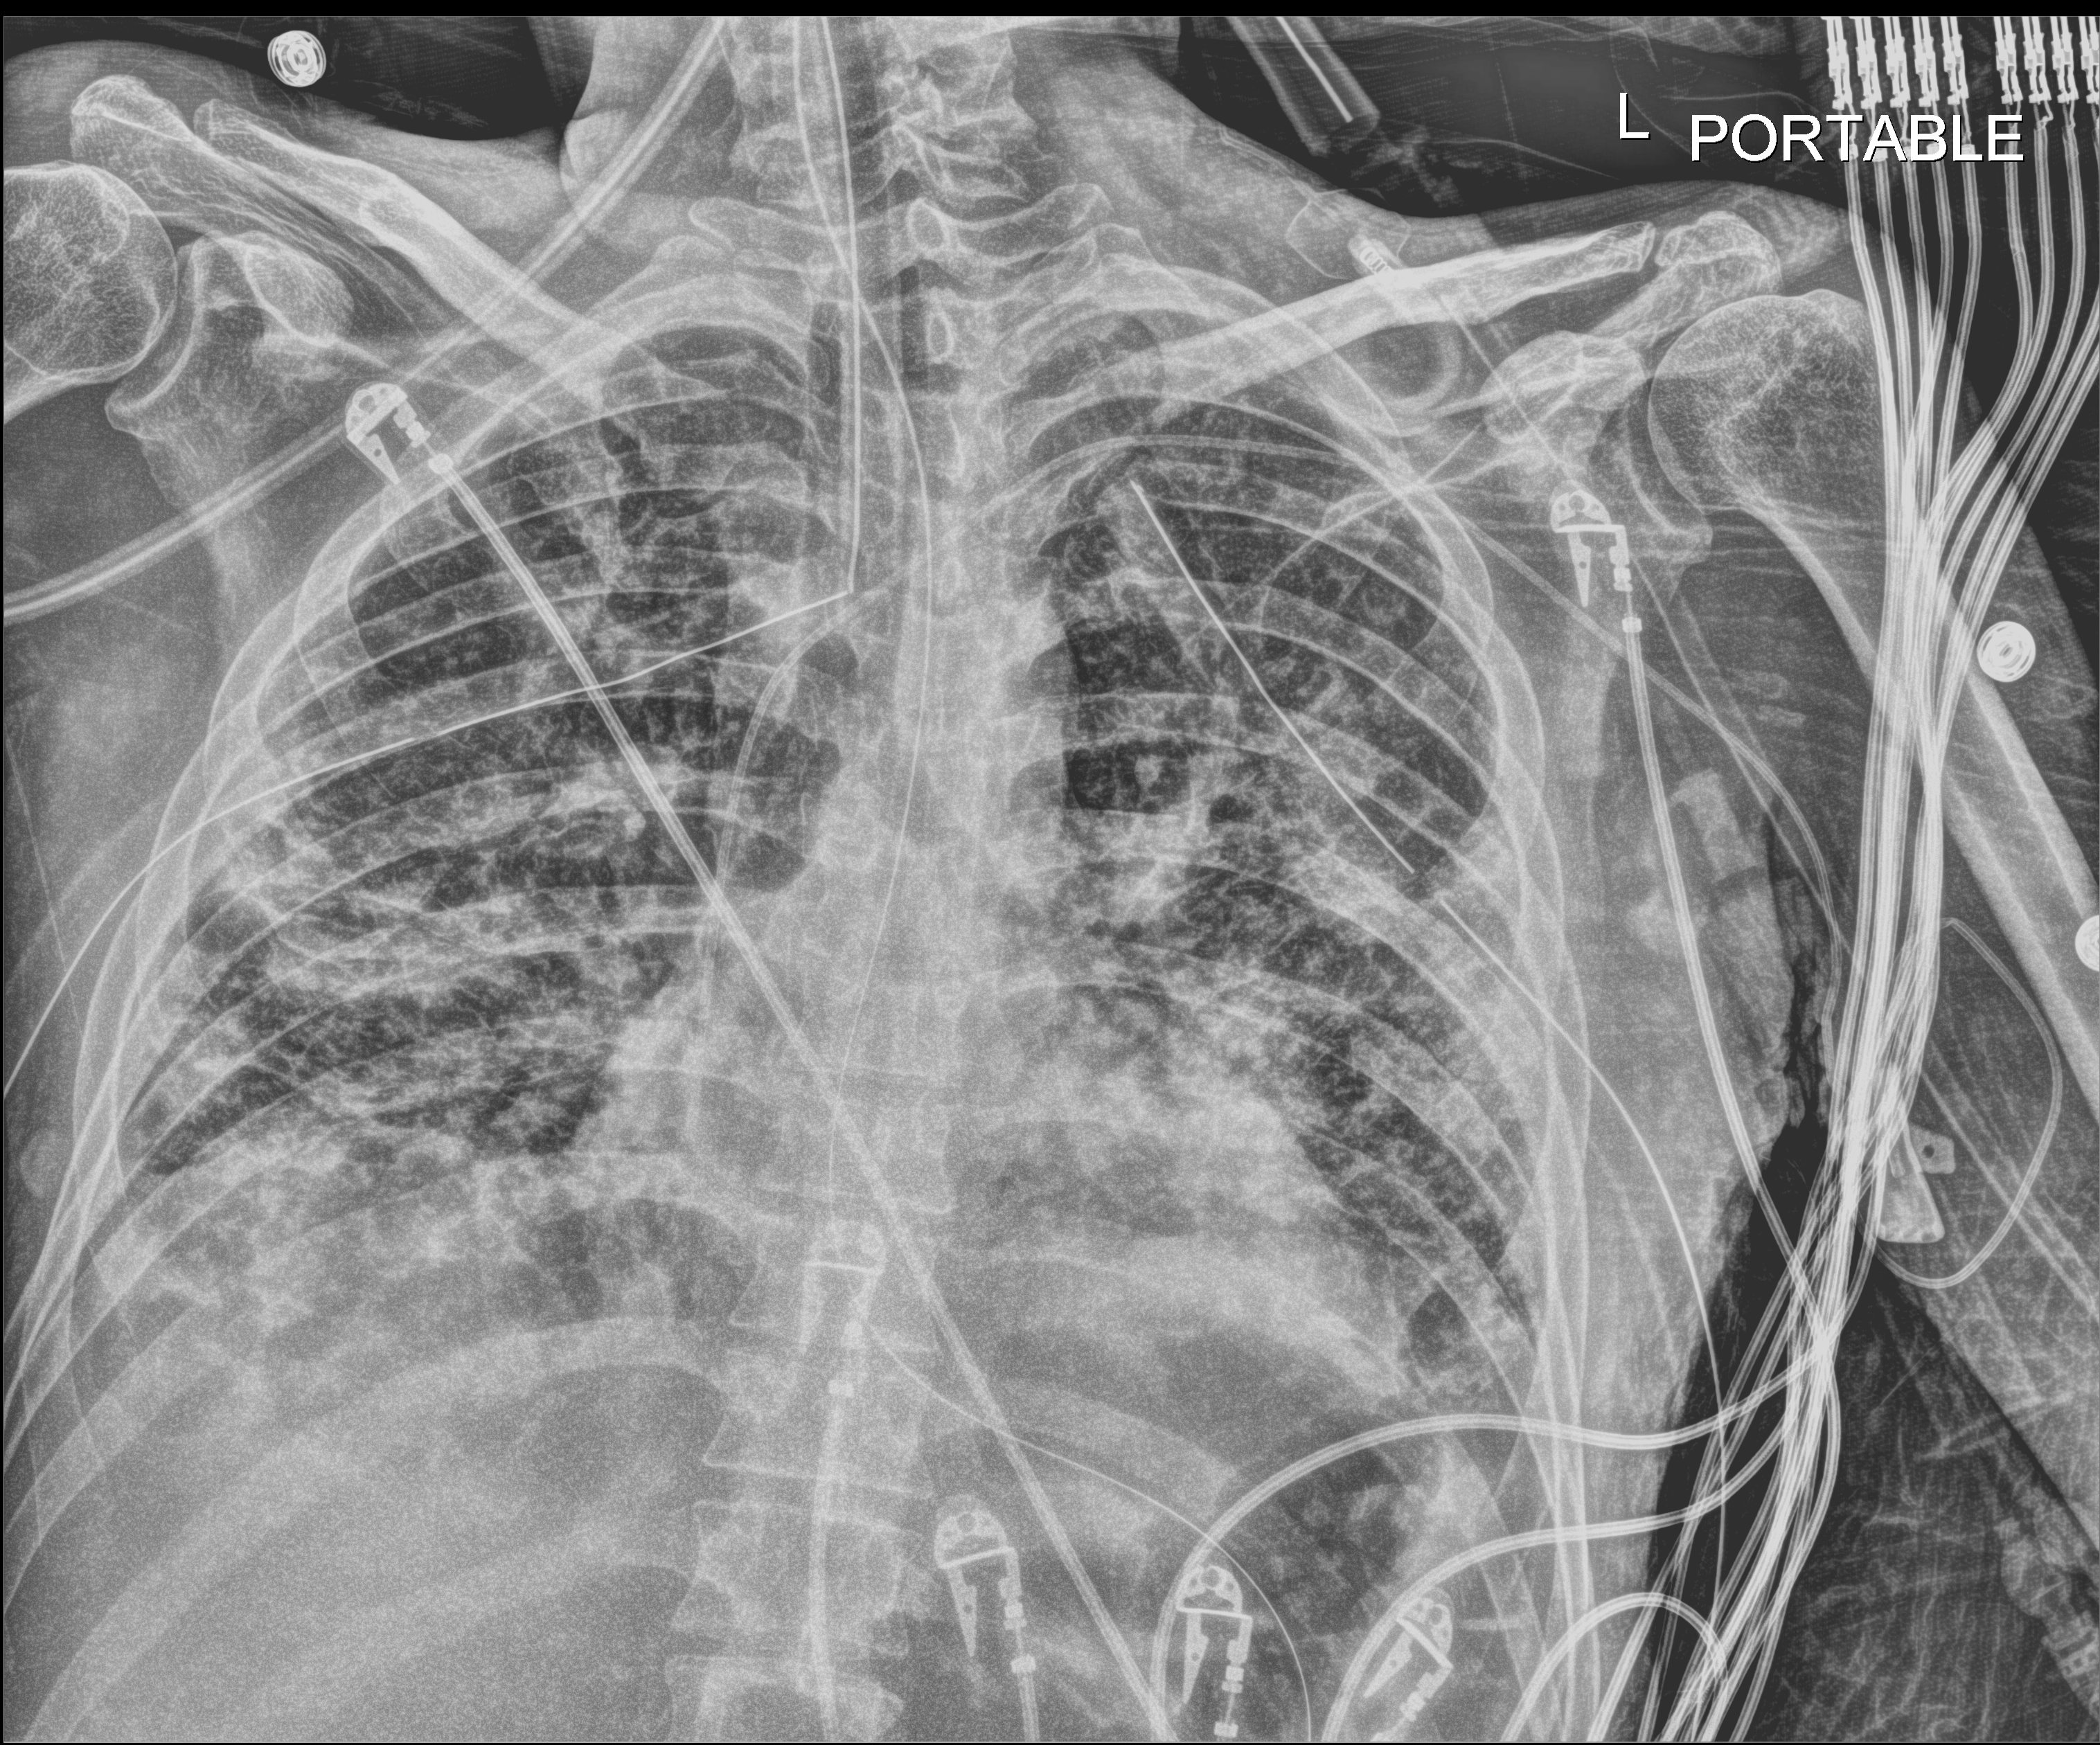
Portable chest radiograph; anteroposterior (AP) projection. Patient hospitalised with COVID-19; male, aged 18–59 years.
Admission-level facts for this patient (not findings on this image; timing relative to this image not recorded):
- mechanically ventilated during this hospital stay: yes
- admitted to intensive care during this hospital stay: yes